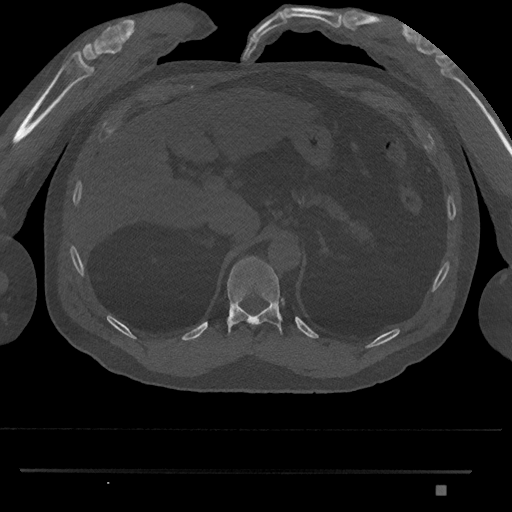
CT including the spine, one axial slice; position 949 of 1134 along the scan axis; reconstruction kernel Br40s/3; 120 kVp; bone window (W 1800 / L 400 HU); 512 × 512 image matrix. Male patient, age 65 years. From the clinical record (not read from this slice): primary cancer: prostate.
Outlined on this slice (semi-automatically segmented with operator editing):
- T11 vertebra: bounding box <226,256,283,335> (left, top, right, bottom; pixels)